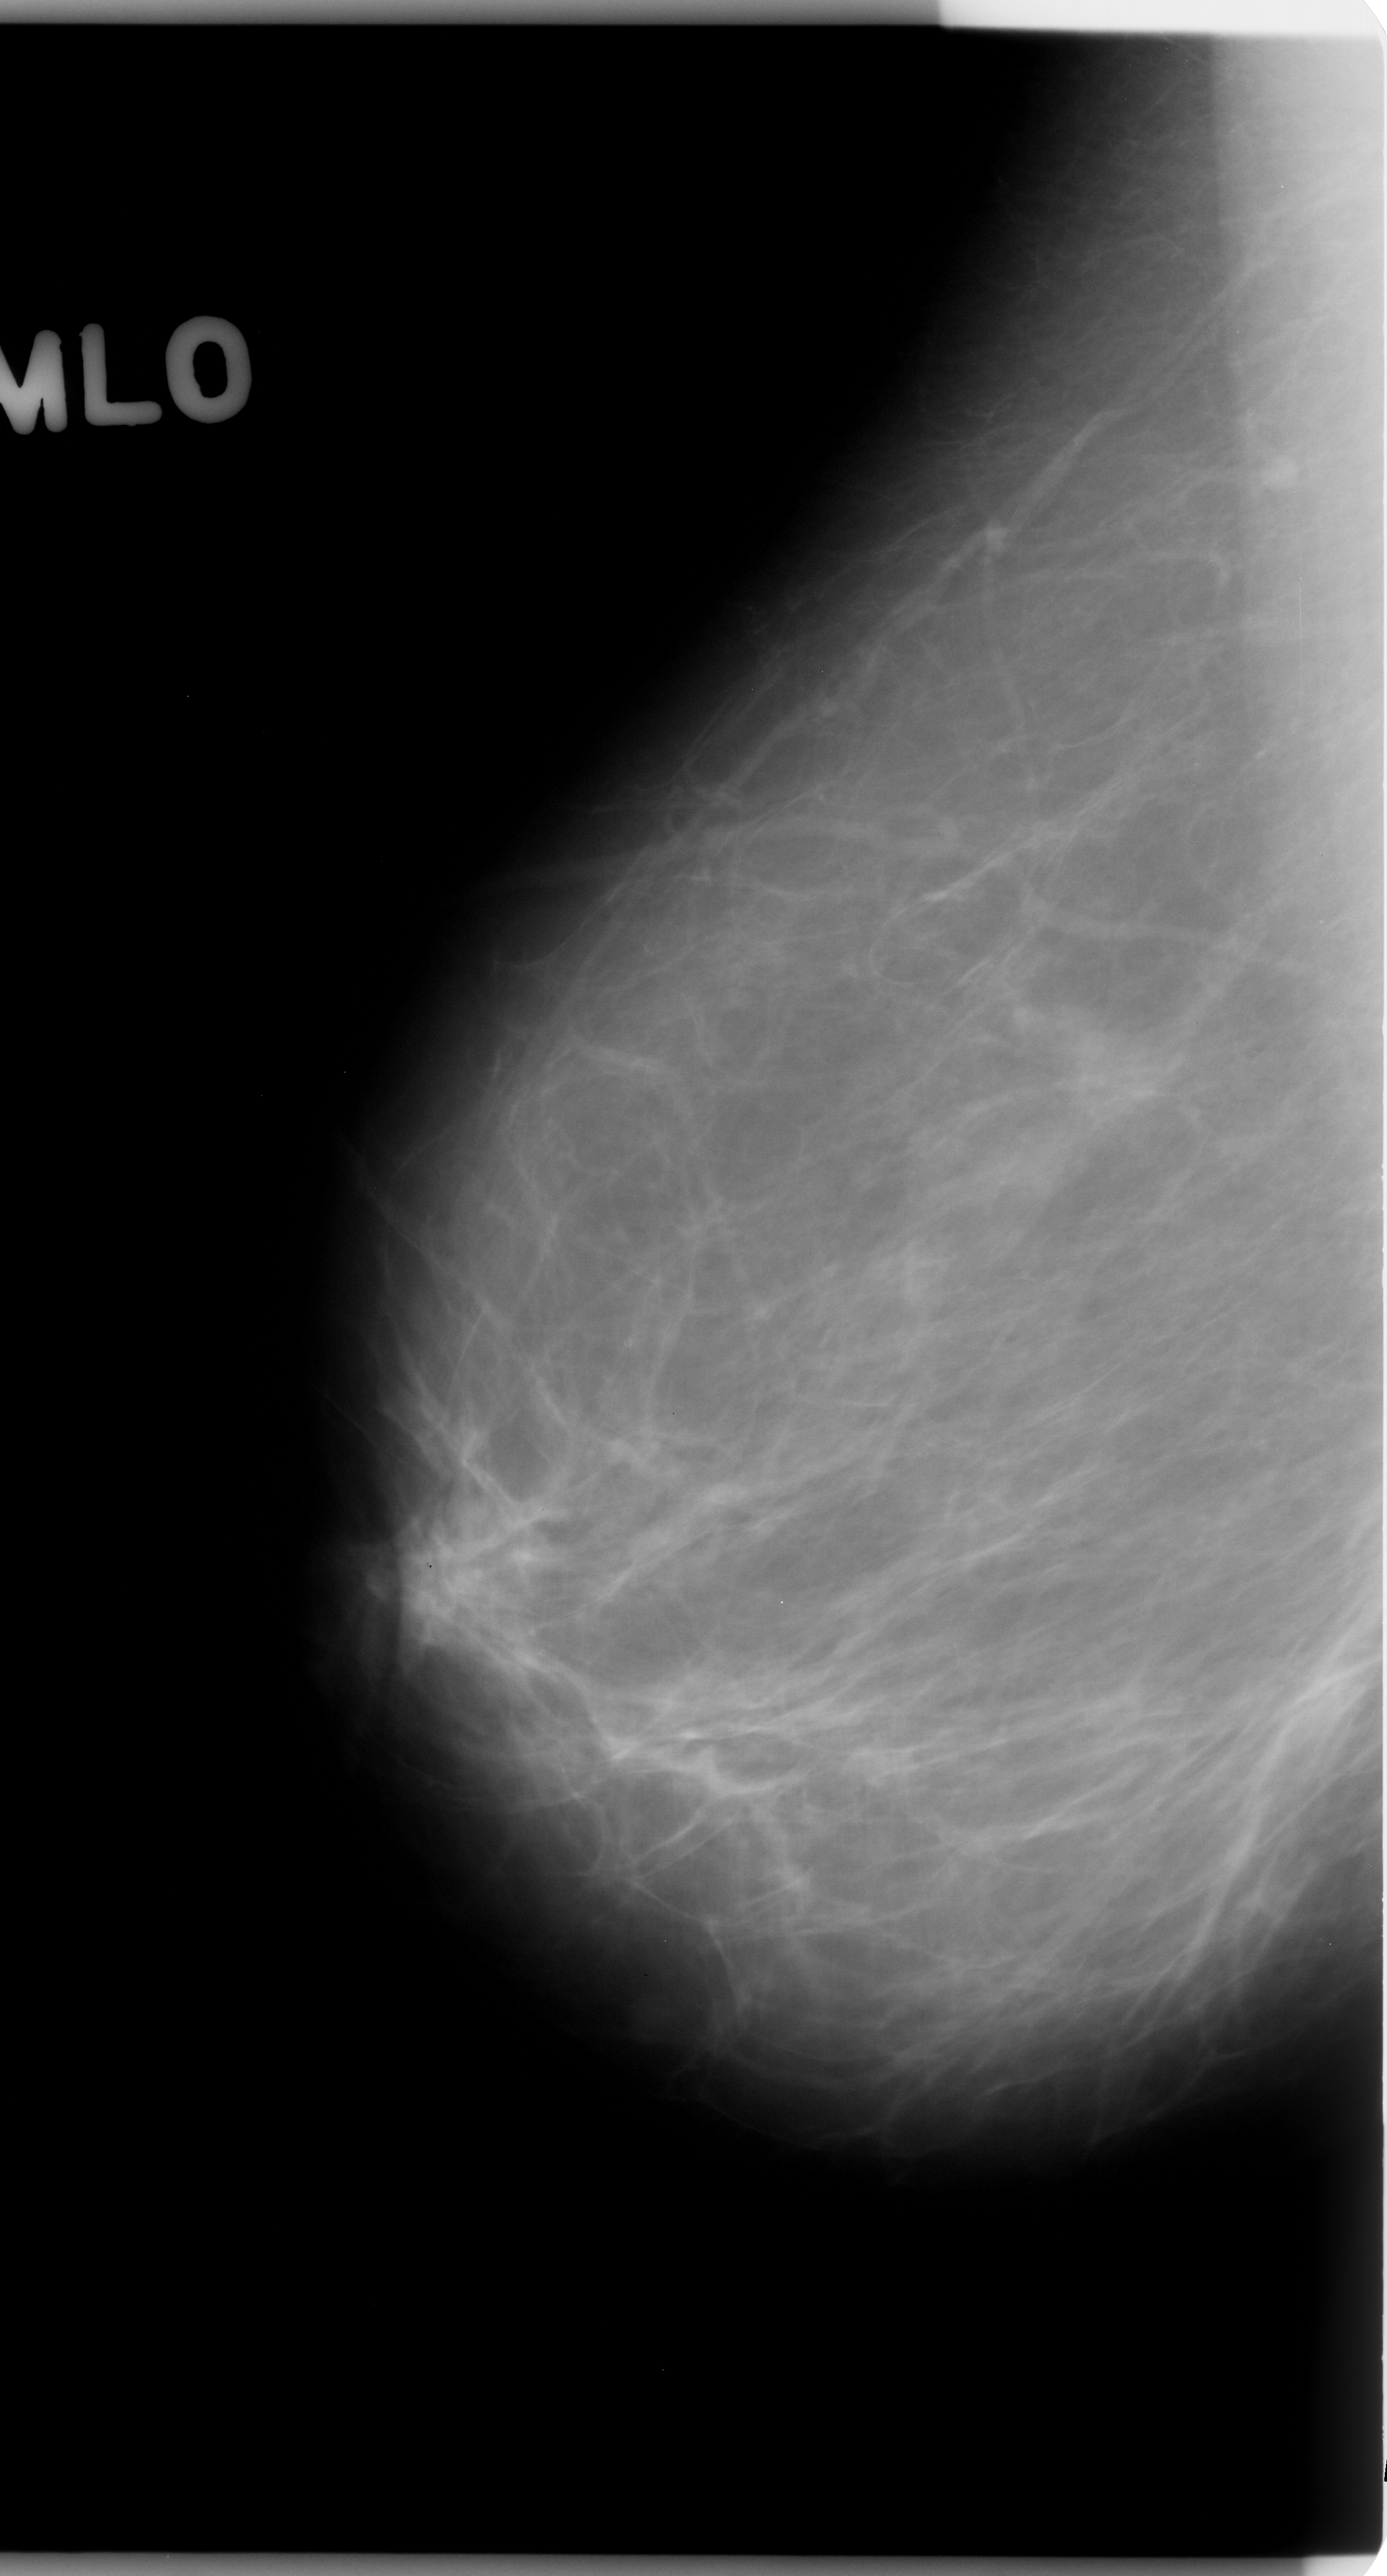
Mammogram (digitized film); right breast; mediolateral oblique (MLO) view; breast composition: almost entirely fatty (BI-RADS density category 1 of 4).
Radiologist-marked abnormalities on this image: mass, shape lobulated, margins ill defined; BI-RADS assessment category 5; pathology (as recorded): malignant.